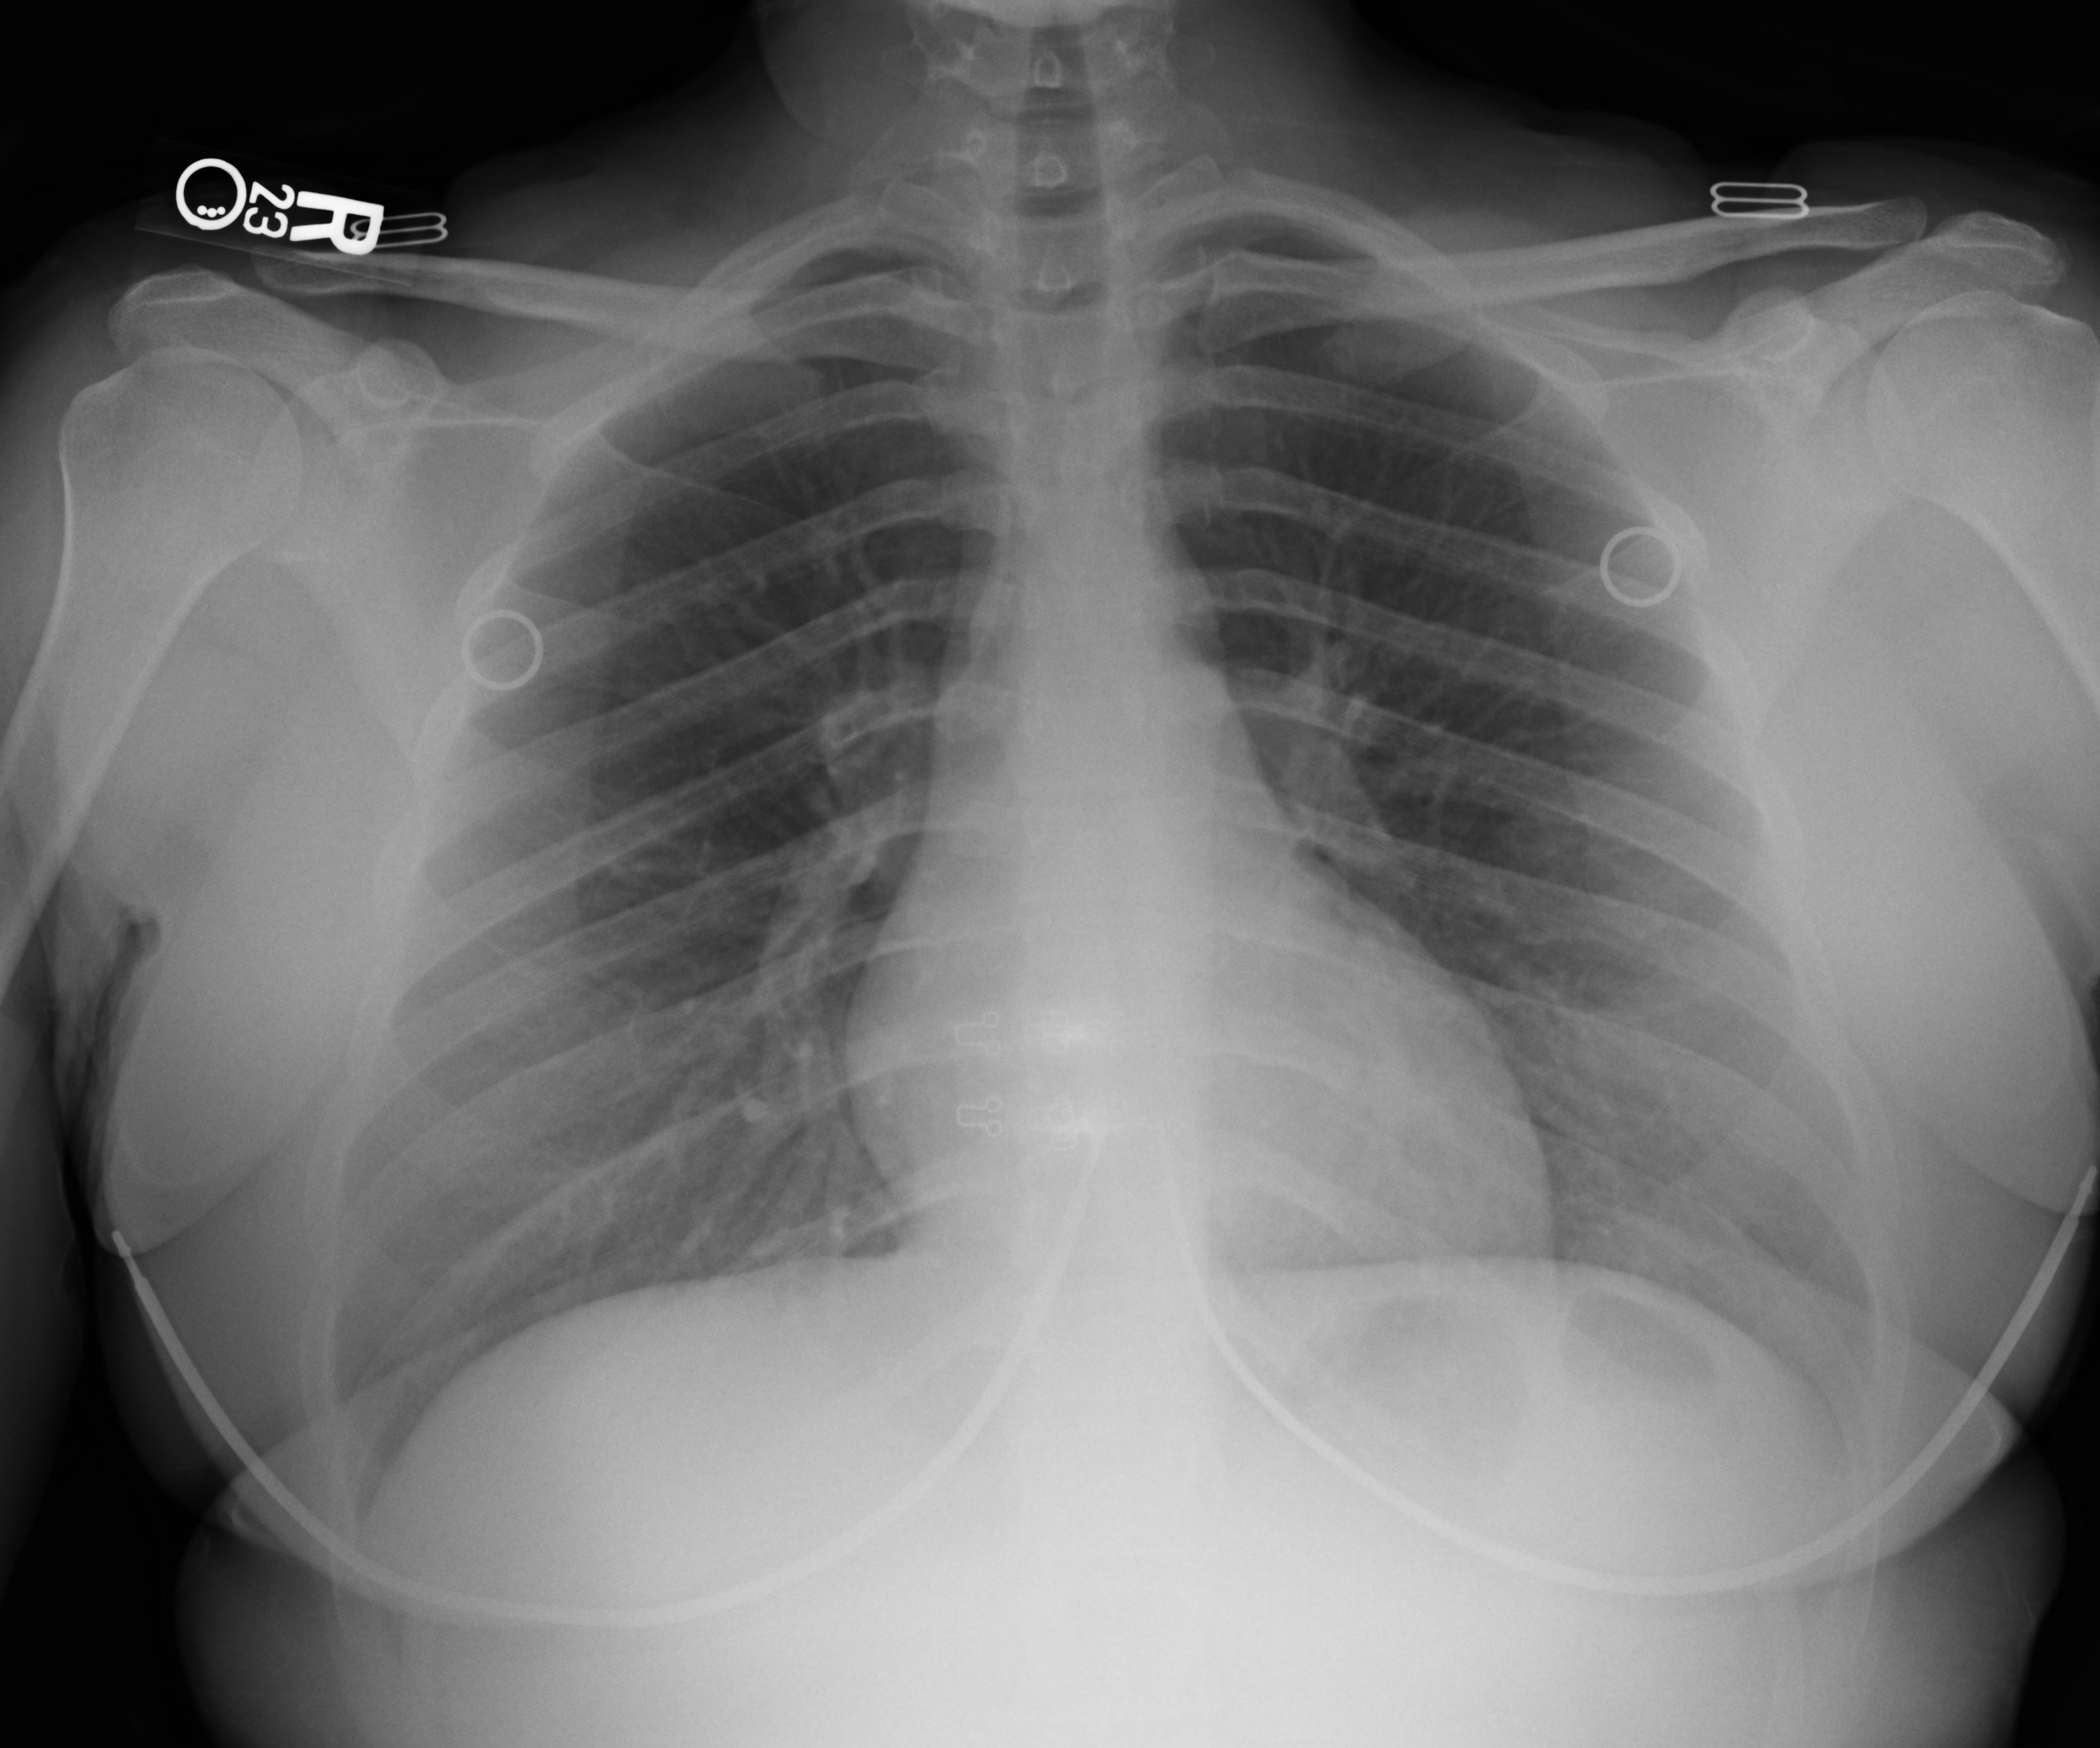
Chest X-ray (portable); anteroposterior (AP) projection. Patient hospitalised with COVID-19; female, aged 18–59 years.
Hospital-stay facts (about this admission, not read from this image; timing relative to this image not recorded):
- mechanically ventilated during this hospital stay: no